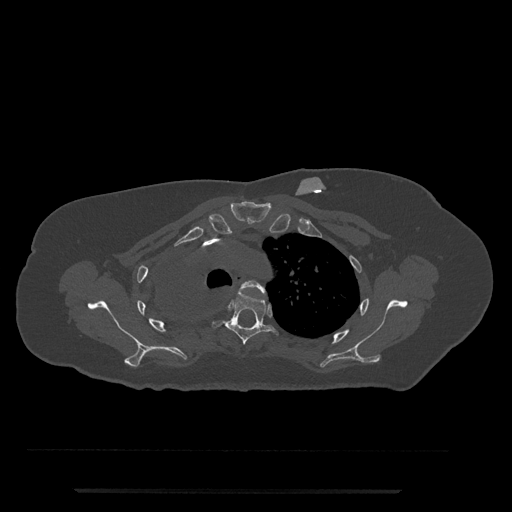
CT including the spine, one axial slice; slice 594 of 797 in the series (ordered by position); reconstruction kernel Br40s/3; 120 kVp; bone window (W 1800 / L 400 HU); 0.5 mm slice thickness; 512 × 512 image matrix, field of view 440 × 440 mm. Patient: female, 51 years. From the clinical record (not read from this slice): primary cancer: neuro.
Structures marked on this image (semi-automatically segmented with operator editing):
- T3 vertebra: box from (x=240, y=280) to (x=266, y=295) px
- T4 vertebra: (x=213, y=291)–(x=279, y=345)